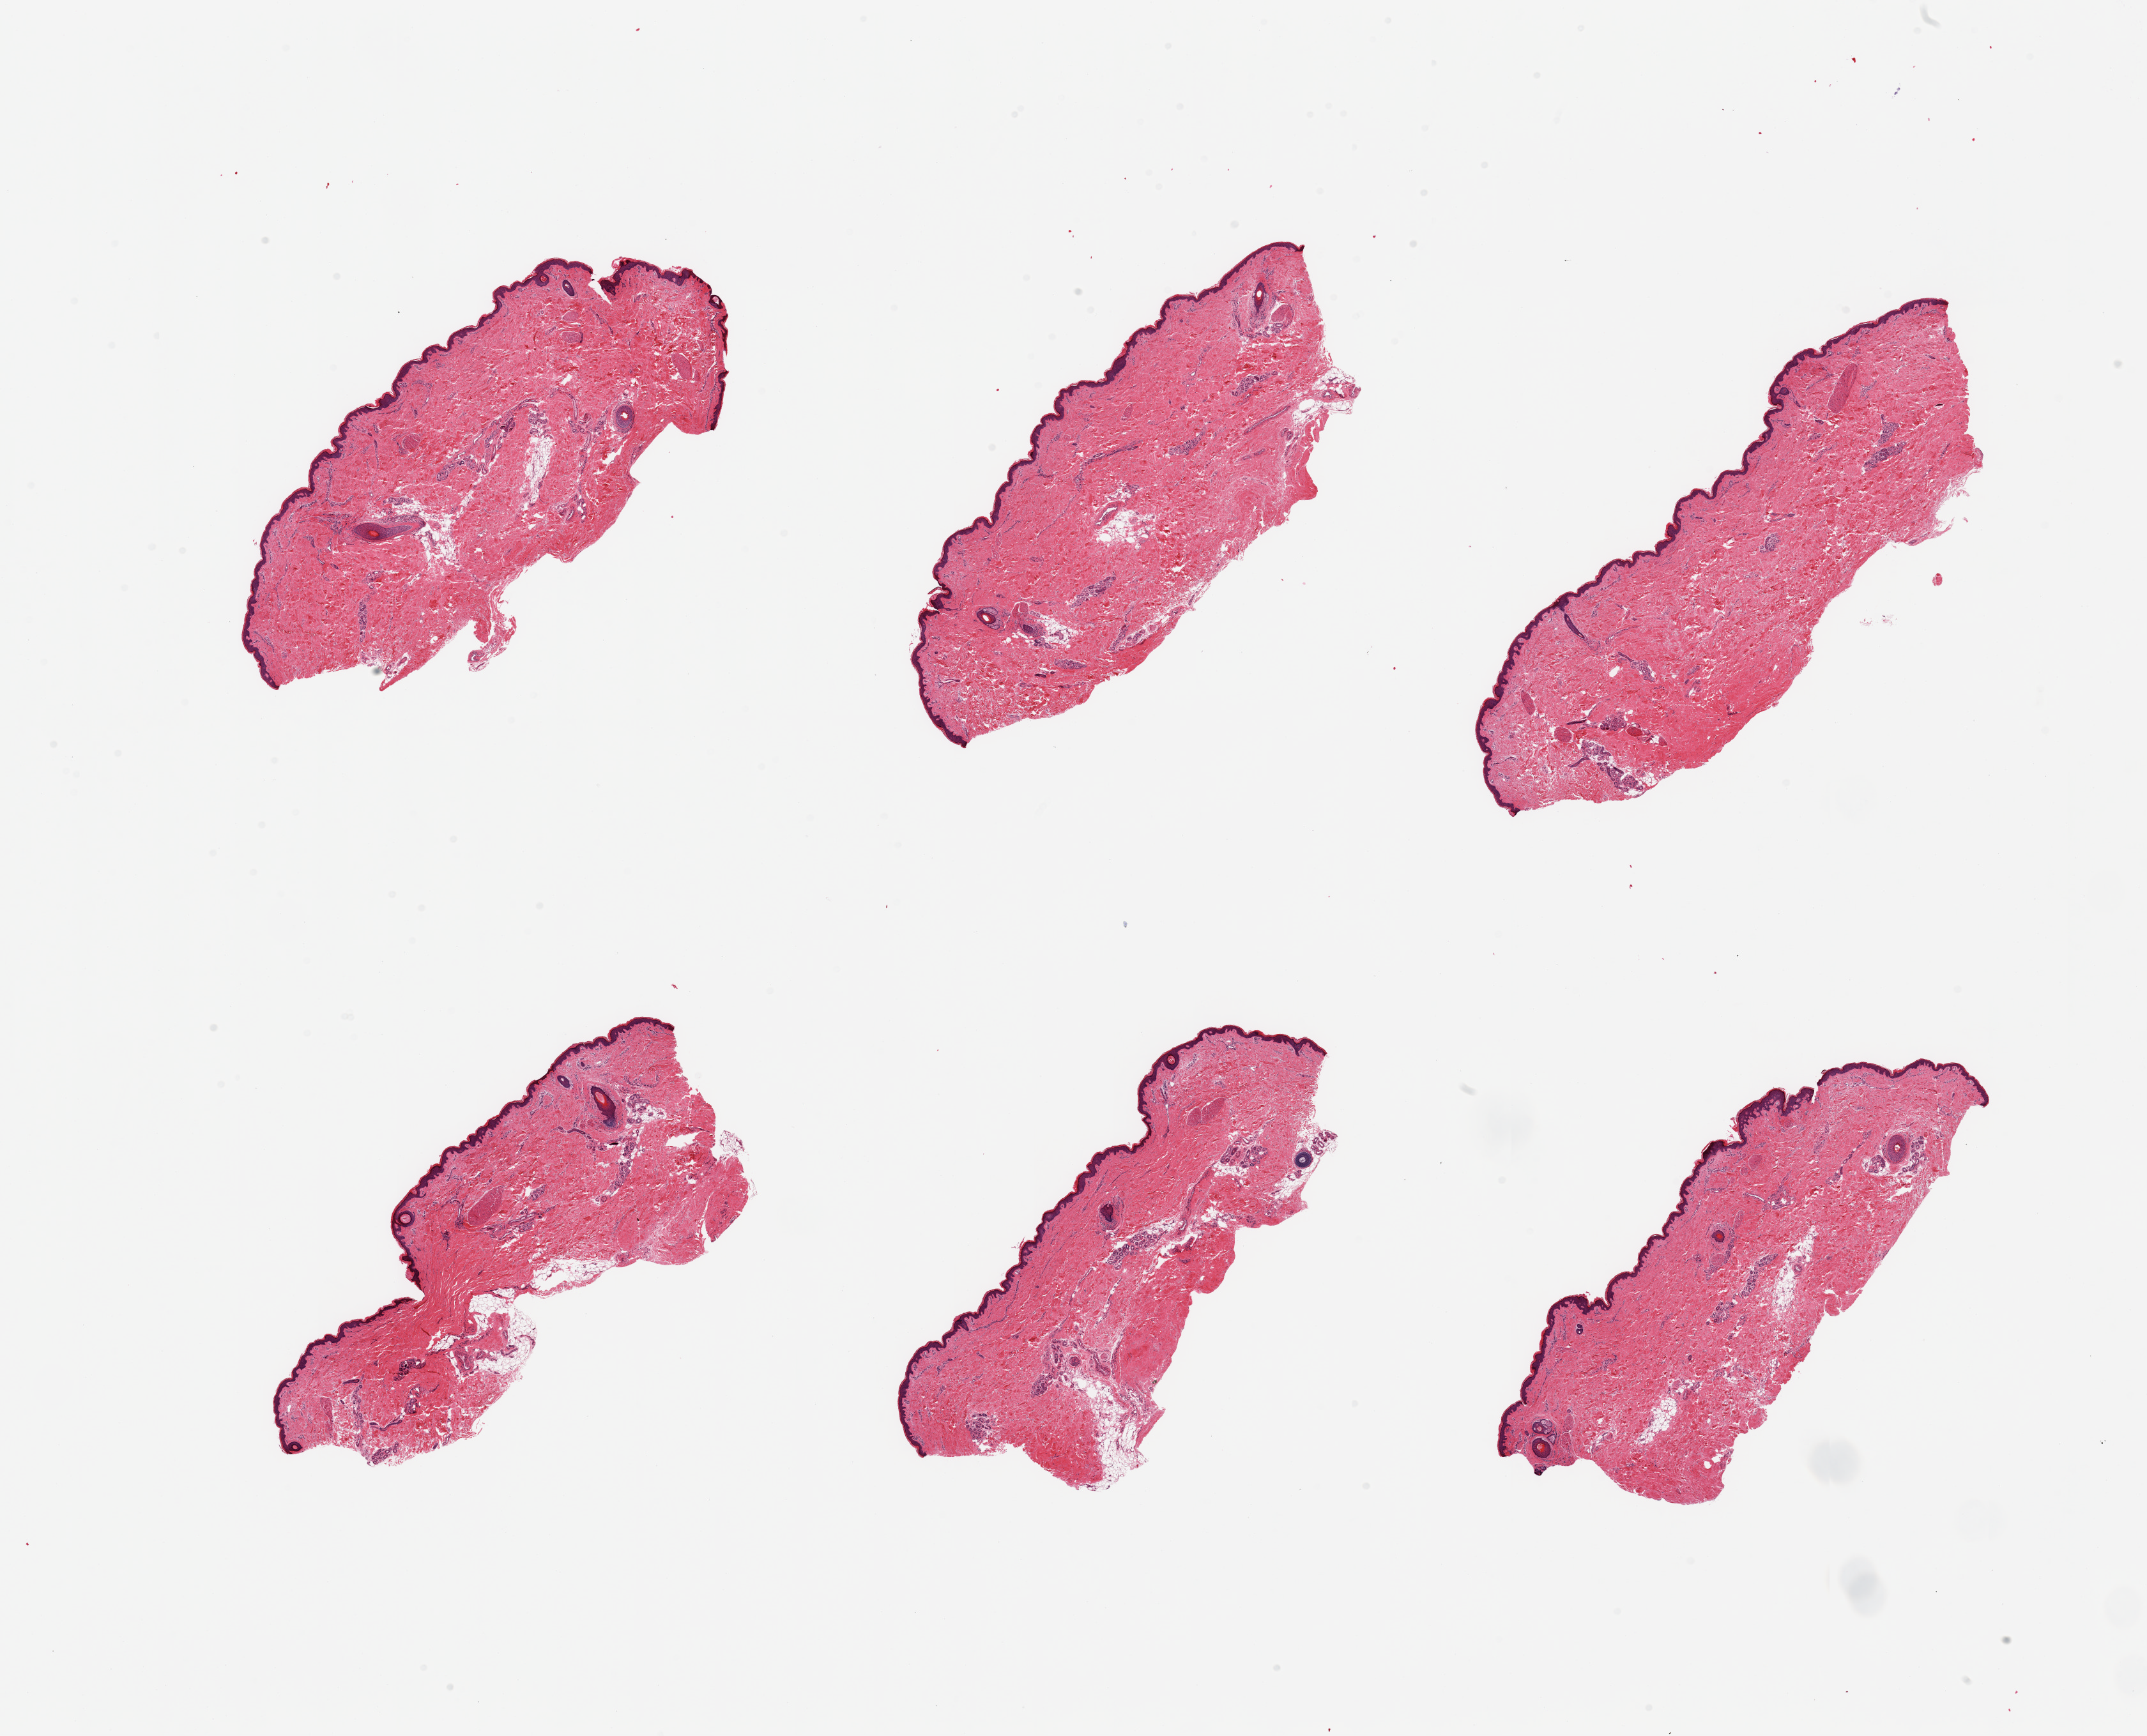
Hematoxylin and eosin (H&E) whole-slide image, low-resolution overview of the scanned area, about 26.6 x 21.5 mm; PAXgene-fixed, paraffin-embedded tissue; target tissue: skin of lower leg; tissue donor sample. Donor sex: male.
Reviewer comment on this tissue sample: 6 pieces; well trimmed; 5% intradermal fat.